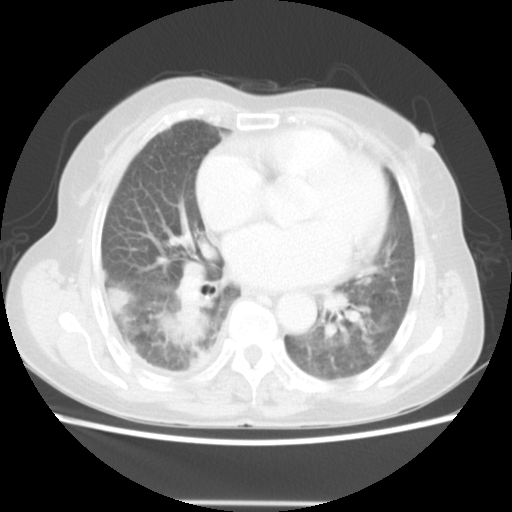
Chest CT, one axial slice. Position 24 of 52 along the scan axis. Reconstruction kernel STANDARD. 140 kVp. Lung window (W 1500 / L -600 HU). 5 mm slice thickness. 512 × 512 image matrix. Patient: female, 67 years. Case-level facts recorded for this patient, not image findings: clinical TNM (as recorded): T3 N1 M1.
Outlined on this slice (rectangle marked by the reading radiologist):
- lung tumour (recorded histology: adenocarcinoma): bounding box <166,295,212,362> (left, top, right, bottom; pixels)